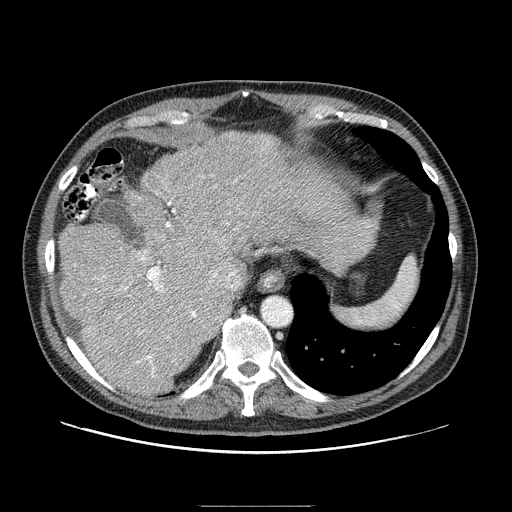
Contrast-enhanced abdominal CT (liver protocol), one axial slice. Slice 66 of 99 in the series (ordered by position). Reconstruction kernel STANDARD. One of 2 acquisitions stored at this slice position. Soft-tissue window (W 400 / L 40 HU). 2.5 mm slice thickness. 512 × 512 image matrix, field of view 400 × 400 mm. From the clinical record (not read from this slice): diagnosis: hepatocellular carcinoma (patient treated with transarterial chemoembolisation; whether this scan precedes or follows treatment is not stated here); TNM stage (as recorded): Stage-II; Child-Pugh class: A; tumour differentiation: well differentiated; tumour nodularity: multinodular.
Structures marked on this image (semi-automatically segmented with operator editing):
- abdominal aorta: bounding box <263,298,291,326> (left, top, right, bottom; pixels)
- liver parenchyma outside the tumour (the mass and vessels are separate outlines, so this box may not span the whole liver): <58,130,354,396>
- mass: <251,132,281,155>
- liver vessels: <84,176,240,377>